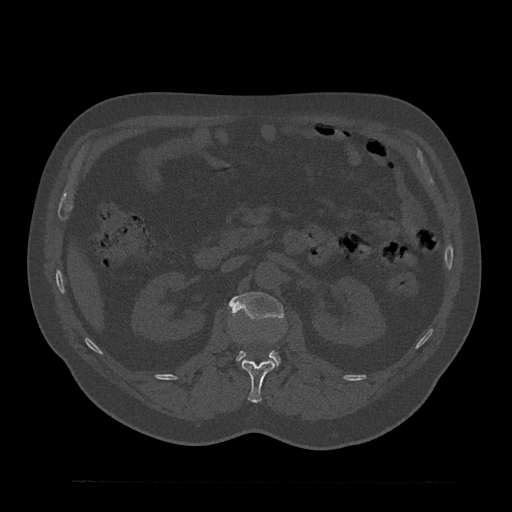
CT including the spine, one axial slice; slice 137 of 797 in the series (ordered by position); reconstruction kernel Br40s/3; 120 kVp; bone window (W 1800 / L 400 HU); 0.5 mm slice thickness; 512 × 512 image matrix. Male patient, age 61 years. From the clinical record (not read from this slice): primary cancer: prostate.
Annotated regions visible in this slice (semi-automatic segmentation, software-assisted and operator-edited):
- L1 vertebra: bounding box [x1, y1, x2, y2] px = [241, 341, 275, 403]
- L2 vertebra: [228, 292, 283, 364]